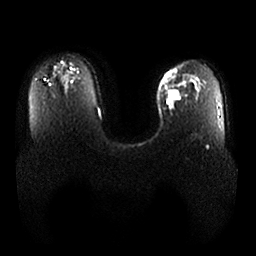
Breast MRI, one axial slice; position 19 of 25 along the scan axis; diffusion-weighted series; image 2 of 4 stored at this slice position (different b-values; order by instance number); 1.5 T; 256 × 256 image matrix, field of view 380 × 380 mm. Female patient.
Outlined on this slice (expert manual segmentation):
- tumour on diffusion-weighted imaging: bounding box [x1, y1, x2, y2] px = [167, 88, 180, 102]